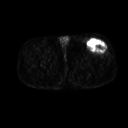
FDG PET of an extremity soft-tissue mass (from a PET/CT study), one axial slice; position 247 of 267 along the scan axis; 3.27 mm slice thickness; 128 × 128 image matrix, field of view 500 × 500 mm. Male patient, age 64 years. From the clinical record (not read from this slice): histological type: extraskeletal osteosarcoma; grade: high; site of the primary tumour: thigh.
Annotated regions visible in this slice (expert contour drawn on MRI and transferred to this co-registered scan by the dataset authors):
- gross tumour volume (mass): bounding box [x1, y1, x2, y2] px = [88, 40, 107, 52]